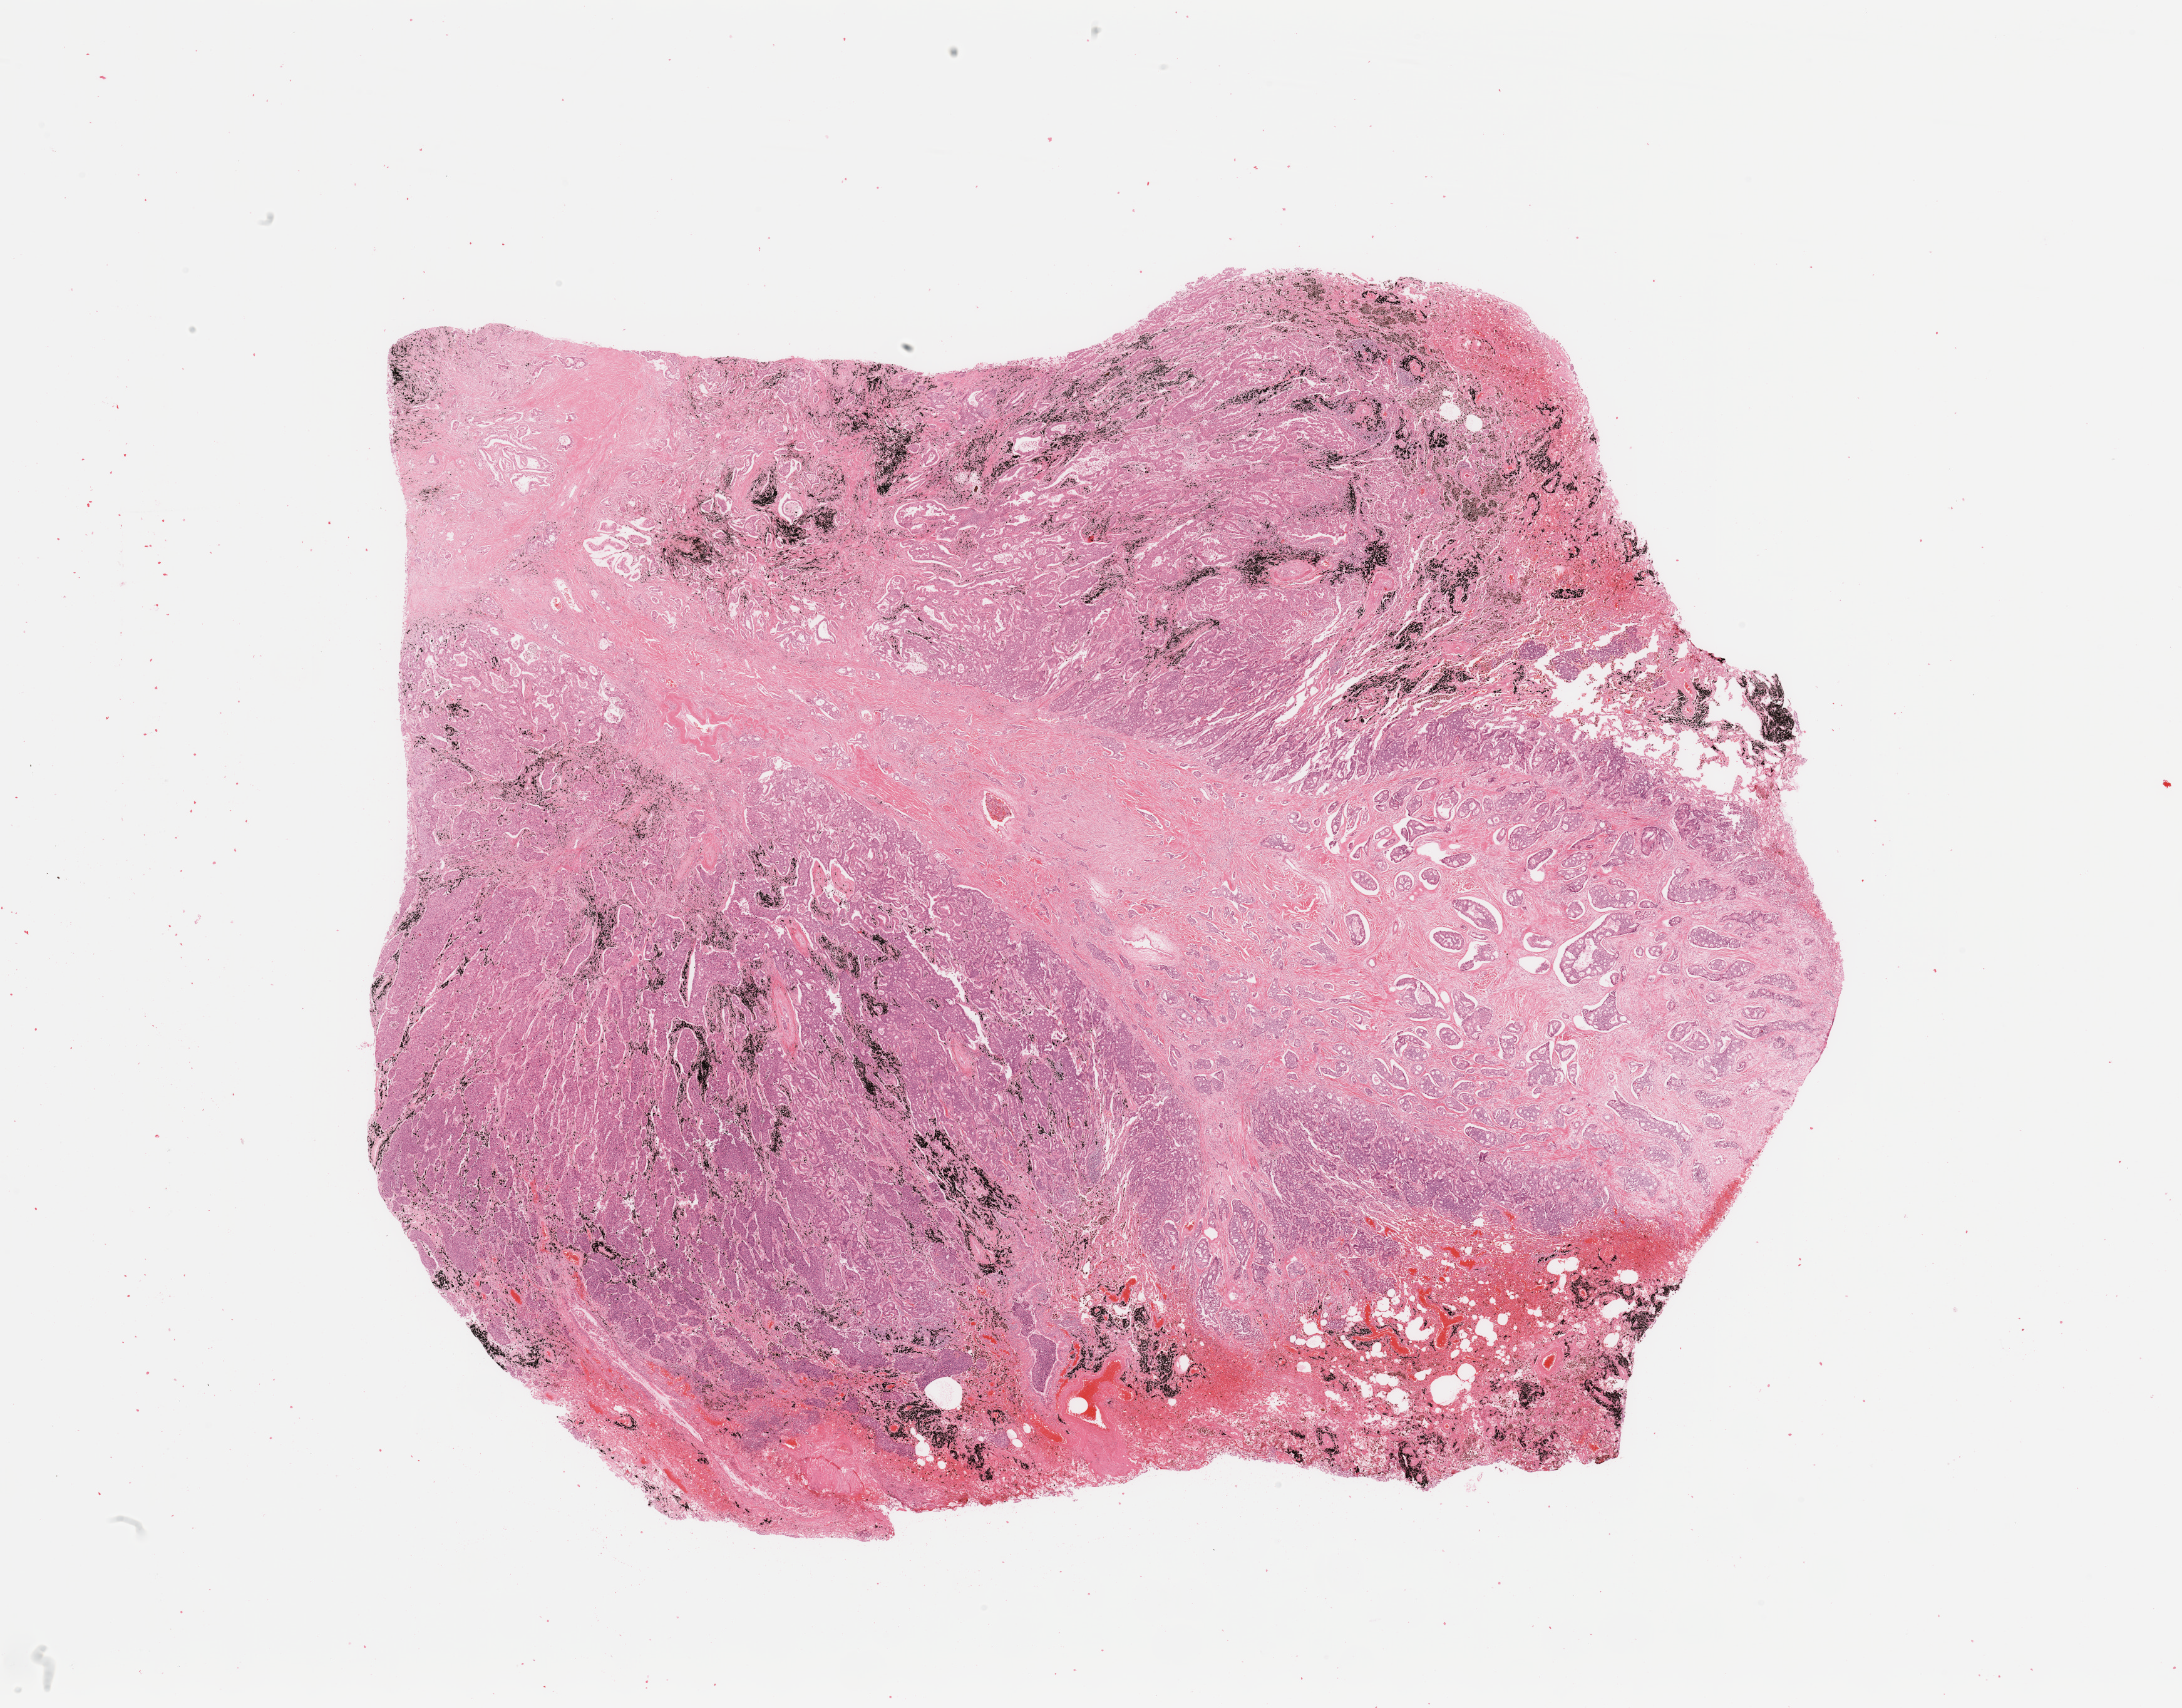
Digitized H&E tissue section (whole slide), low-resolution overview of the scanned area, about 27.6 x 21.6 mm, lung, tumour tissue. 56-year-old male patient.
Diagnosis: Adenocarcinoma, NOS.